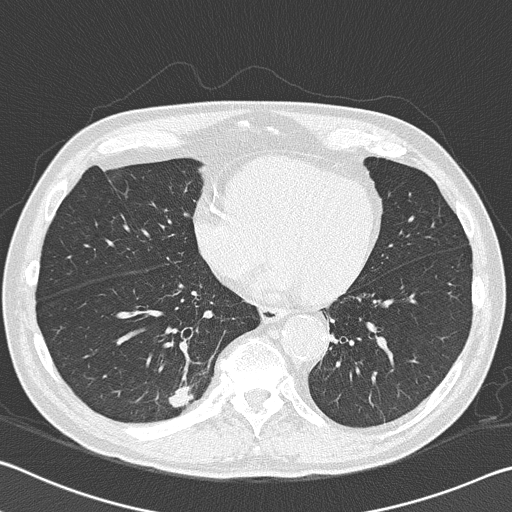
Chest CT (low-dose screening protocol), one axial image; first (baseline) screen; lung window (W 1500 / L -600 HU); 2 mm slice thickness; 120 kVp; slice 114 of 168 in the series; 512 × 512 image matrix, field of view 340 × 340 mm. Male, age 74 years at enrolment.
Expert-annotated lung lesion, box from (x=148, y=368) to (x=214, y=428) px. Reader record for this screening exam (exam-level; its link to the box is not recorded): non-calcified nodule or mass ≥4 mm, right lower lobe, 13 × 11 mm, spiculated (stellate) margins, soft tissue attenuation.